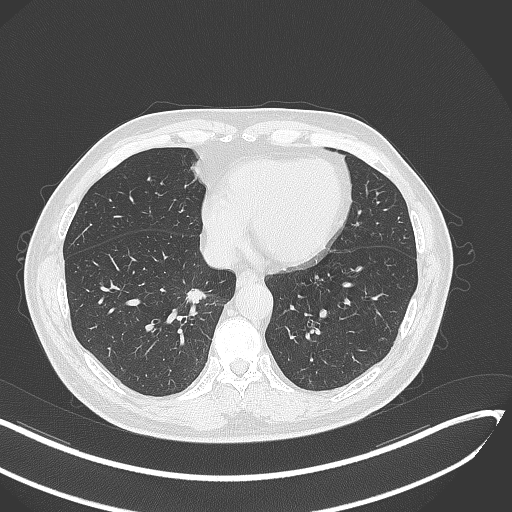
Chest CT, one axial slice. Position 125 of 429 along the scan axis. Lung window (W 1500 / L -600 HU). 1 mm slice thickness. 512 × 512 image matrix. Male patient, age 62 years. Case-level facts recorded for this patient, not image findings: clinical TNM (as recorded): T1b N0 M0; histopathological grade: G2.
Structures marked on this image (rectangle marked by the reading radiologist):
- lung tumour (recorded histology: adenocarcinoma): box from (x=184, y=288) to (x=211, y=309) px